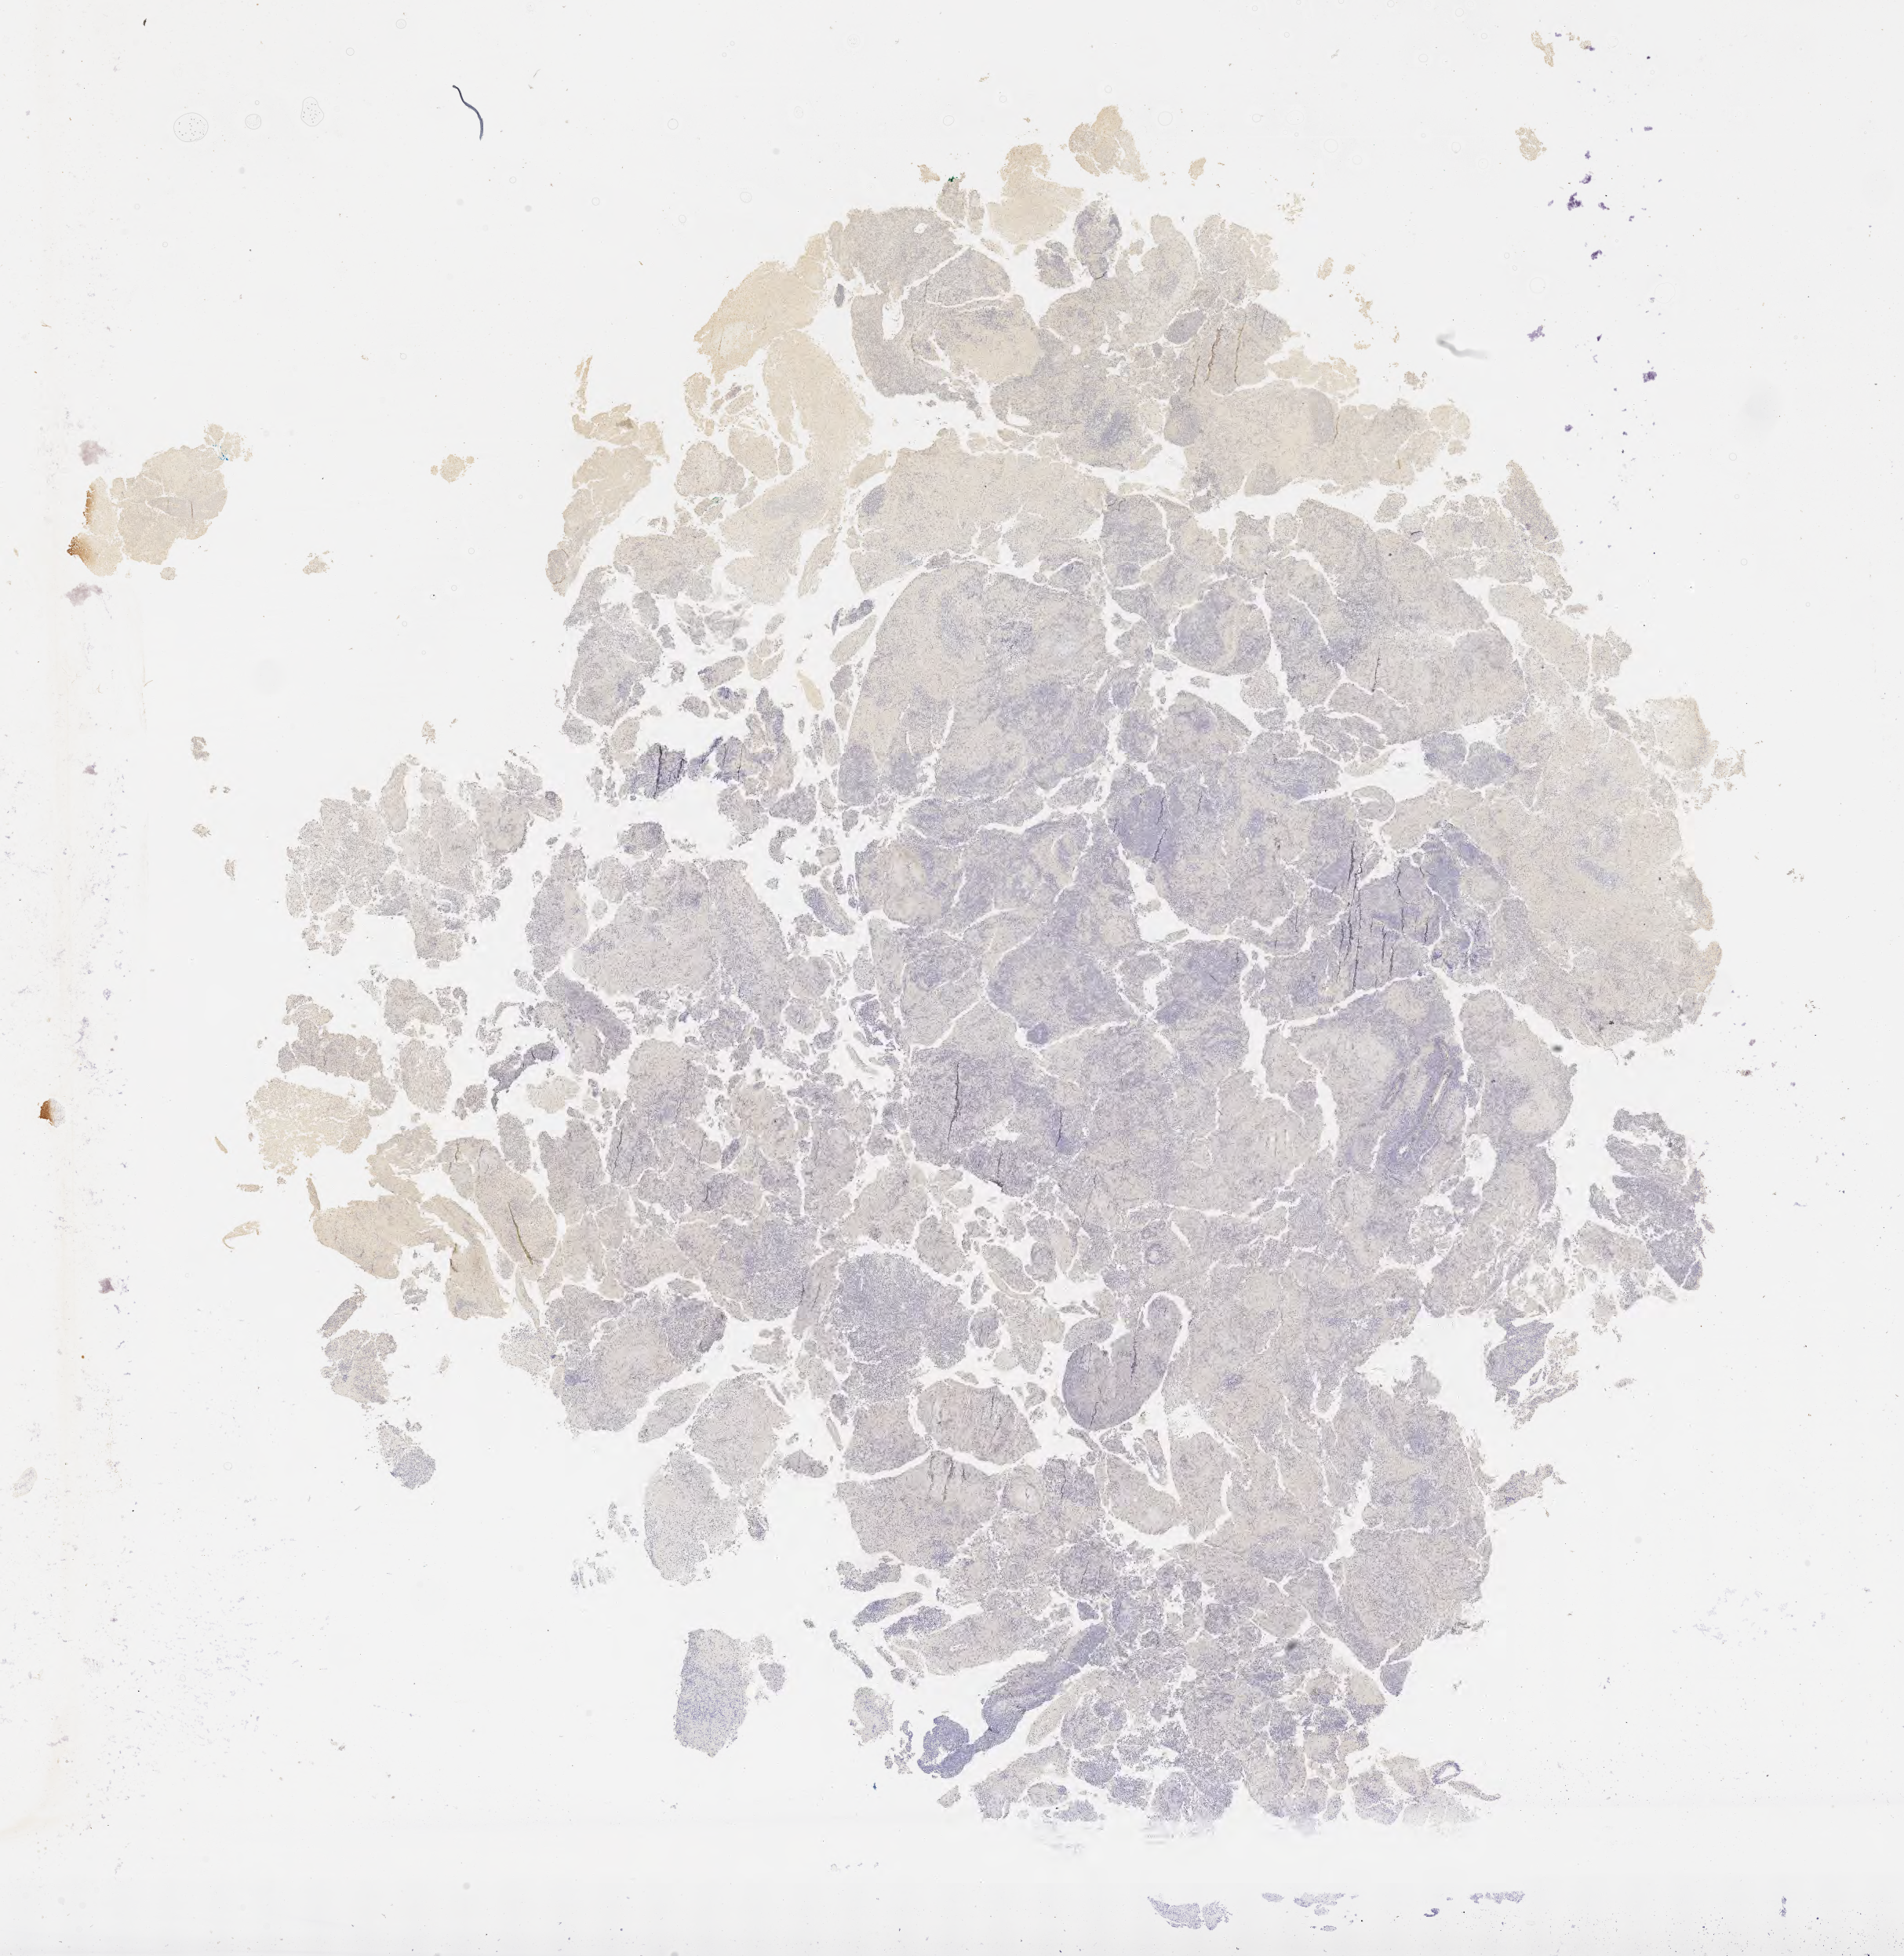
Immunohistochemistry (IHC) whole-slide image stained for BCL6, low-resolution overview of the scanned area, about 19.6 x 20.2 mm, specimen: tumor tissue, anatomic site: brain. Patient male; aged 51.
* diagnosis: Diffuse large B-cell lymphoma, NOS